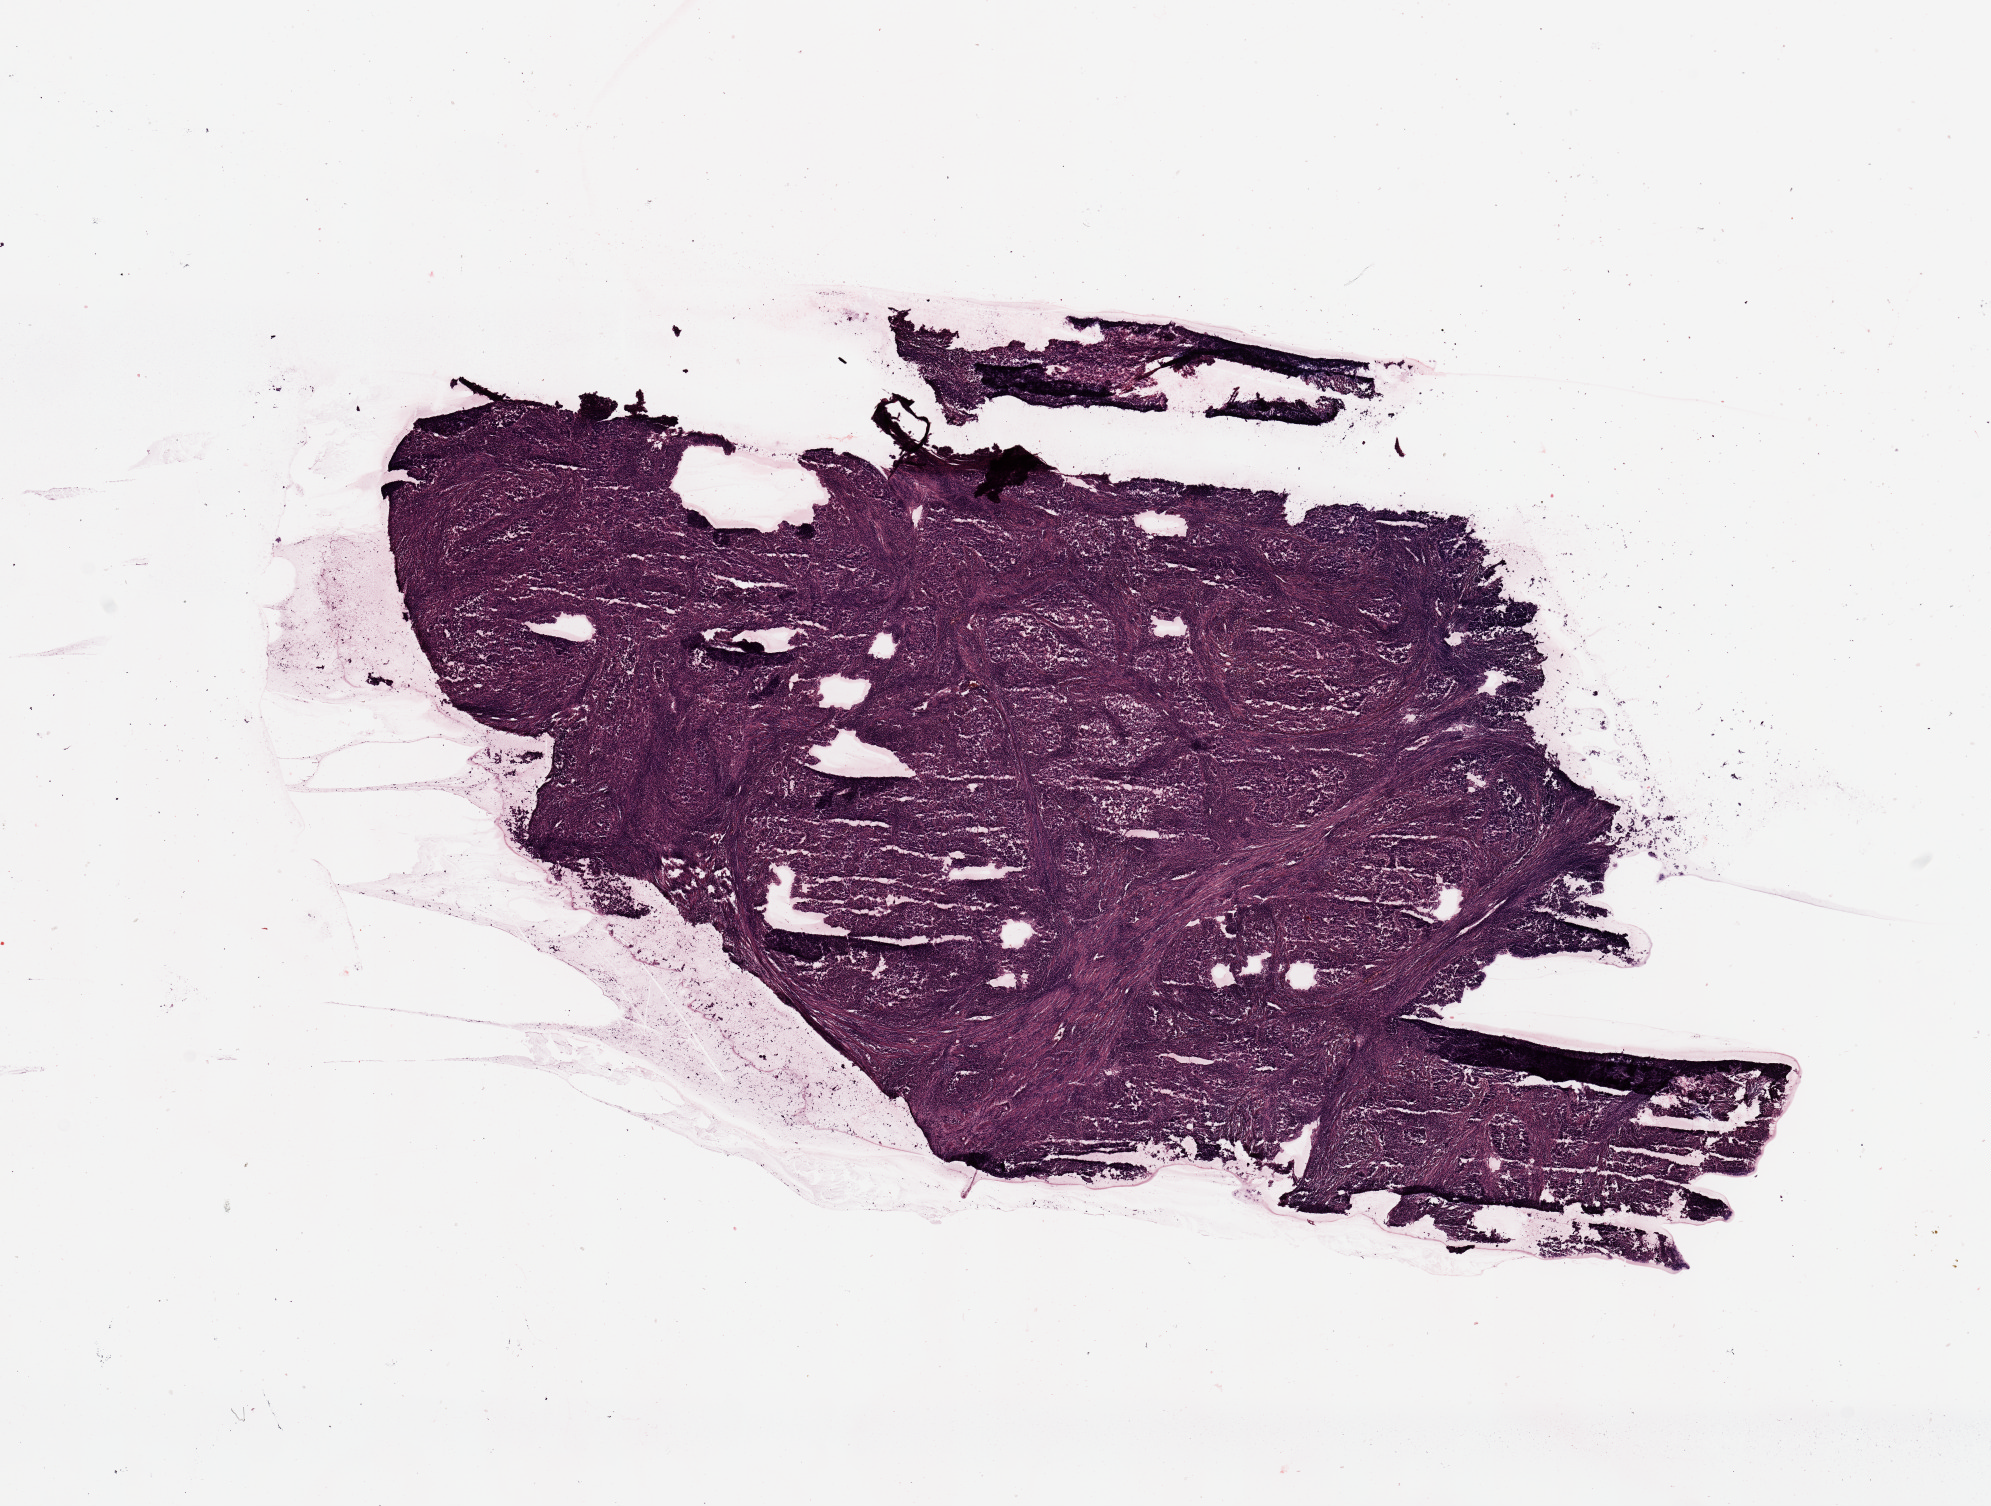
Digitized Hematoxylin and eosin (H&E) stained tissue section (whole slide), whole scanned area (about 15.8 x 11.9 mm) shown as a low-resolution overview. Tumour tissue sample, uterus. Patient: female, age 62 years. Histologic grade: G3 (poorly differentiated).
AJCC pathologic stage: I. Histologic diagnosis: Endometrioid adenocarcinoma, NOS.